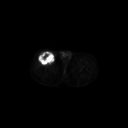
FDG PET of an extremity soft-tissue mass (from a PET/CT study), one axial slice; slice 283 of 311 in the series (ordered by position); 3.27 mm slice thickness; 128 × 128 image matrix, field of view 700 × 700 mm. Male patient, age 56 years. Case-level facts recorded for this patient, not image findings: histological type: pleiomorphic leiomyosarcoma; grade: intermediate; site of the primary tumour: right thigh.
Annotated regions visible in this slice (expert contour drawn on MRI and transferred to this co-registered scan by the dataset authors):
- gross tumour volume including surrounding oedema: bounding box (x1, y1, x2, y2) in pixels: (38, 52, 55, 65)
- gross tumour volume (mass): (38, 52, 55, 65)